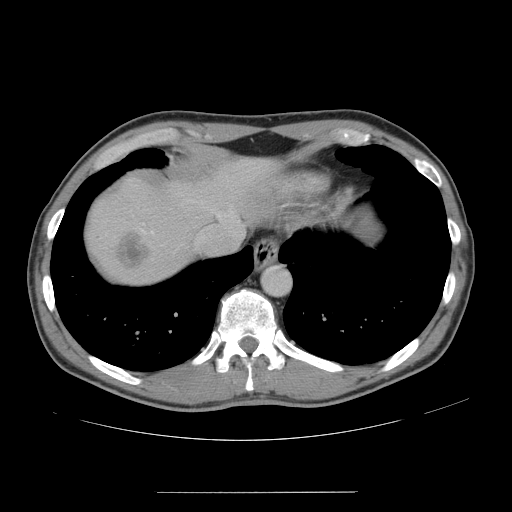
Contrast-enhanced abdominal CT, one axial slice. 120 kVp. Intravenous contrast given. Soft-tissue window (W 400 / L 40 HU). 2.5 mm slice thickness. 512 × 512 image matrix. Male patient, age 53 years. From the clinical record (not read from this slice): diagnosis: colorectal cancer liver metastases, imaged before liver resection; multiple liver metastases: yes; largest metastasis: 2.4 cm; disease in both lobes: no.
Structures marked on this image (manually delineated by an expert):
- hepatic veins: box from (x=205, y=206) to (x=244, y=236) px
- liver: (x=87, y=159)–(x=271, y=282)
- planned liver remnant (the part of the liver to remain after resection): (x=183, y=159)–(x=272, y=218)
- liver metastasis: (x=116, y=233)–(x=147, y=267)